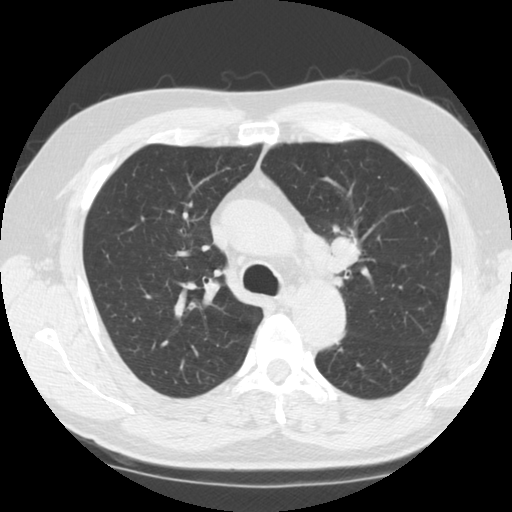
Axial slice from a low-dose chest CT screening exam; third annual screen; lung window (W 1500 / L -600 HU); 2.5 mm slice thickness; standard (soft-tissue) reconstruction kernel (STANDARD); slice 37 of 124 in the series. Male, age 60 years at enrolment. Current smoker at enrolment.
• Expert-annotated lung lesion, box from (x=316, y=223) to (x=369, y=277) px.
• Reader record for this screening exam (exam-level; its link to the box is not recorded): non-calcified nodule or mass ≥4 mm, left upper lobe, 24 × 21 mm, smooth margins, soft tissue attenuation, pre-existing on the prior screen: no.
• Official screen result: positive, other.